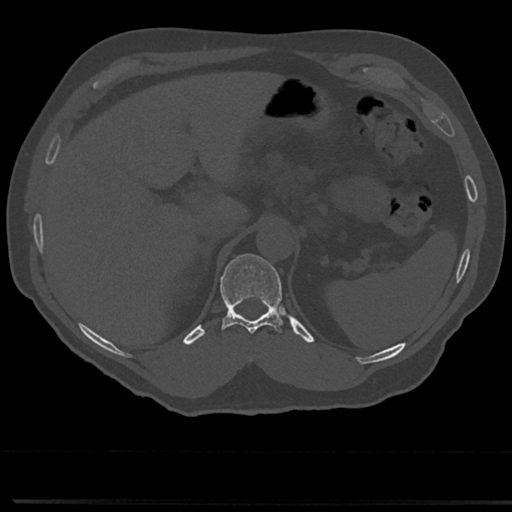
CT including the spine, one axial slice; slice 203 of 817 in the series (ordered by position); bone window (W 1800 / L 400 HU); 0.5 mm slice thickness; 512 × 512 image matrix. Male patient, age 61 years. Case-level facts recorded for this patient, not image findings: primary cancer: prostate.
Structures marked on this image (semi-automatically segmented with operator editing):
- T10 vertebra: bounding box <247,350,254,364> (left, top, right, bottom; pixels)
- T11 vertebra: <220,254,284,332>